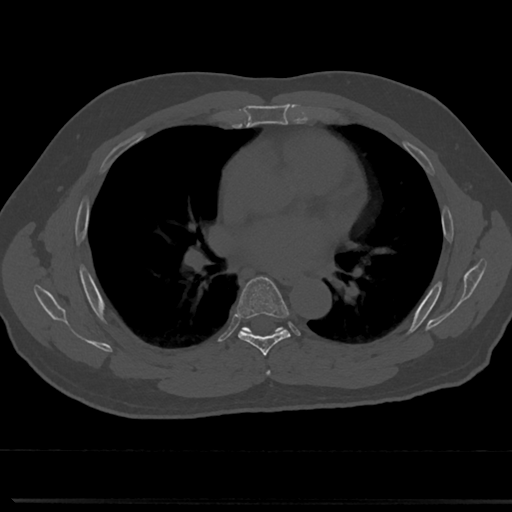
CT including the spine, one axial slice; 120 kVp; bone window (W 1800 / L 400 HU); 0.5 mm slice thickness; 512 × 512 image matrix, field of view 355 × 355 mm. Patient: male, 61 years. Case-level facts recorded for this patient, not image findings: primary cancer: prostate.
Outlined on this slice (semi-automatic segmentation, software-assisted and operator-edited):
- T5 vertebra: bounding box <265,352,273,377> (left, top, right, bottom; pixels)
- T6 vertebra: <219,277,310,354>